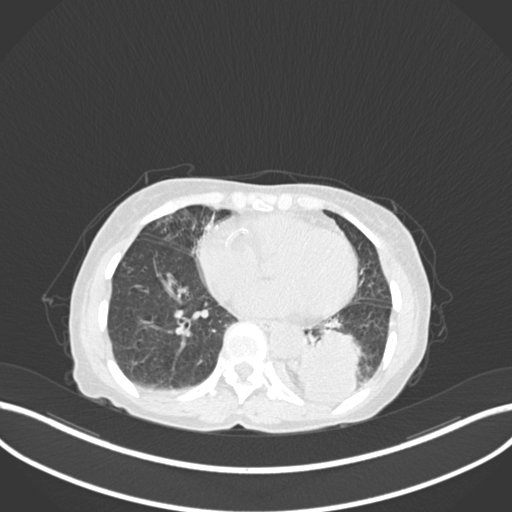
Chest CT, one axial slice; position 44 of 233 along the scan axis; reconstruction kernel B30f; lung window (W 1500 / L -600 HU); 1 mm slice thickness; 512 × 512 image matrix, field of view 400 × 400 mm. Patient: female, 78 years. From the clinical record (not read from this slice): clinical TNM (as recorded): T3 N0 M1.
Structures marked on this image (rectangle marked by the reading radiologist):
- lung tumour (recorded histology: squamous cell carcinoma): bounding box (x1, y1, x2, y2) in pixels: (290, 324, 366, 410)